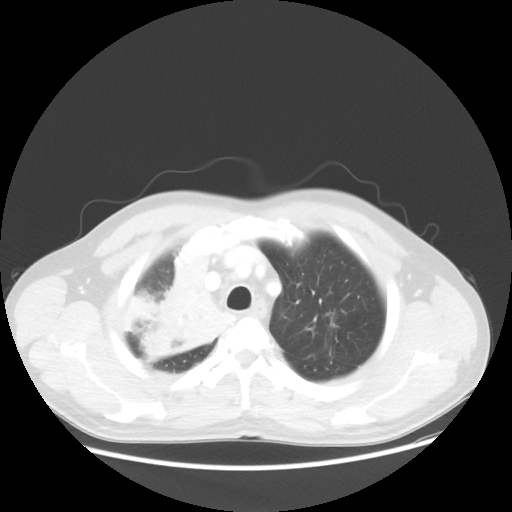
Chest CT, one axial slice; position 44 of 56 along the scan axis; reconstruction kernel STANDARD; lung window (W 1500 / L -600 HU); 512 × 512 image matrix. Male patient, age 60 years. From the clinical record (not read from this slice): clinical TNM (as recorded): T2a N1 M0.
Structures marked on this image (rectangle marked by the reading radiologist):
- lung tumour (recorded histology: squamous cell carcinoma): bounding box (x1, y1, x2, y2) in pixels: (142, 249, 228, 364)